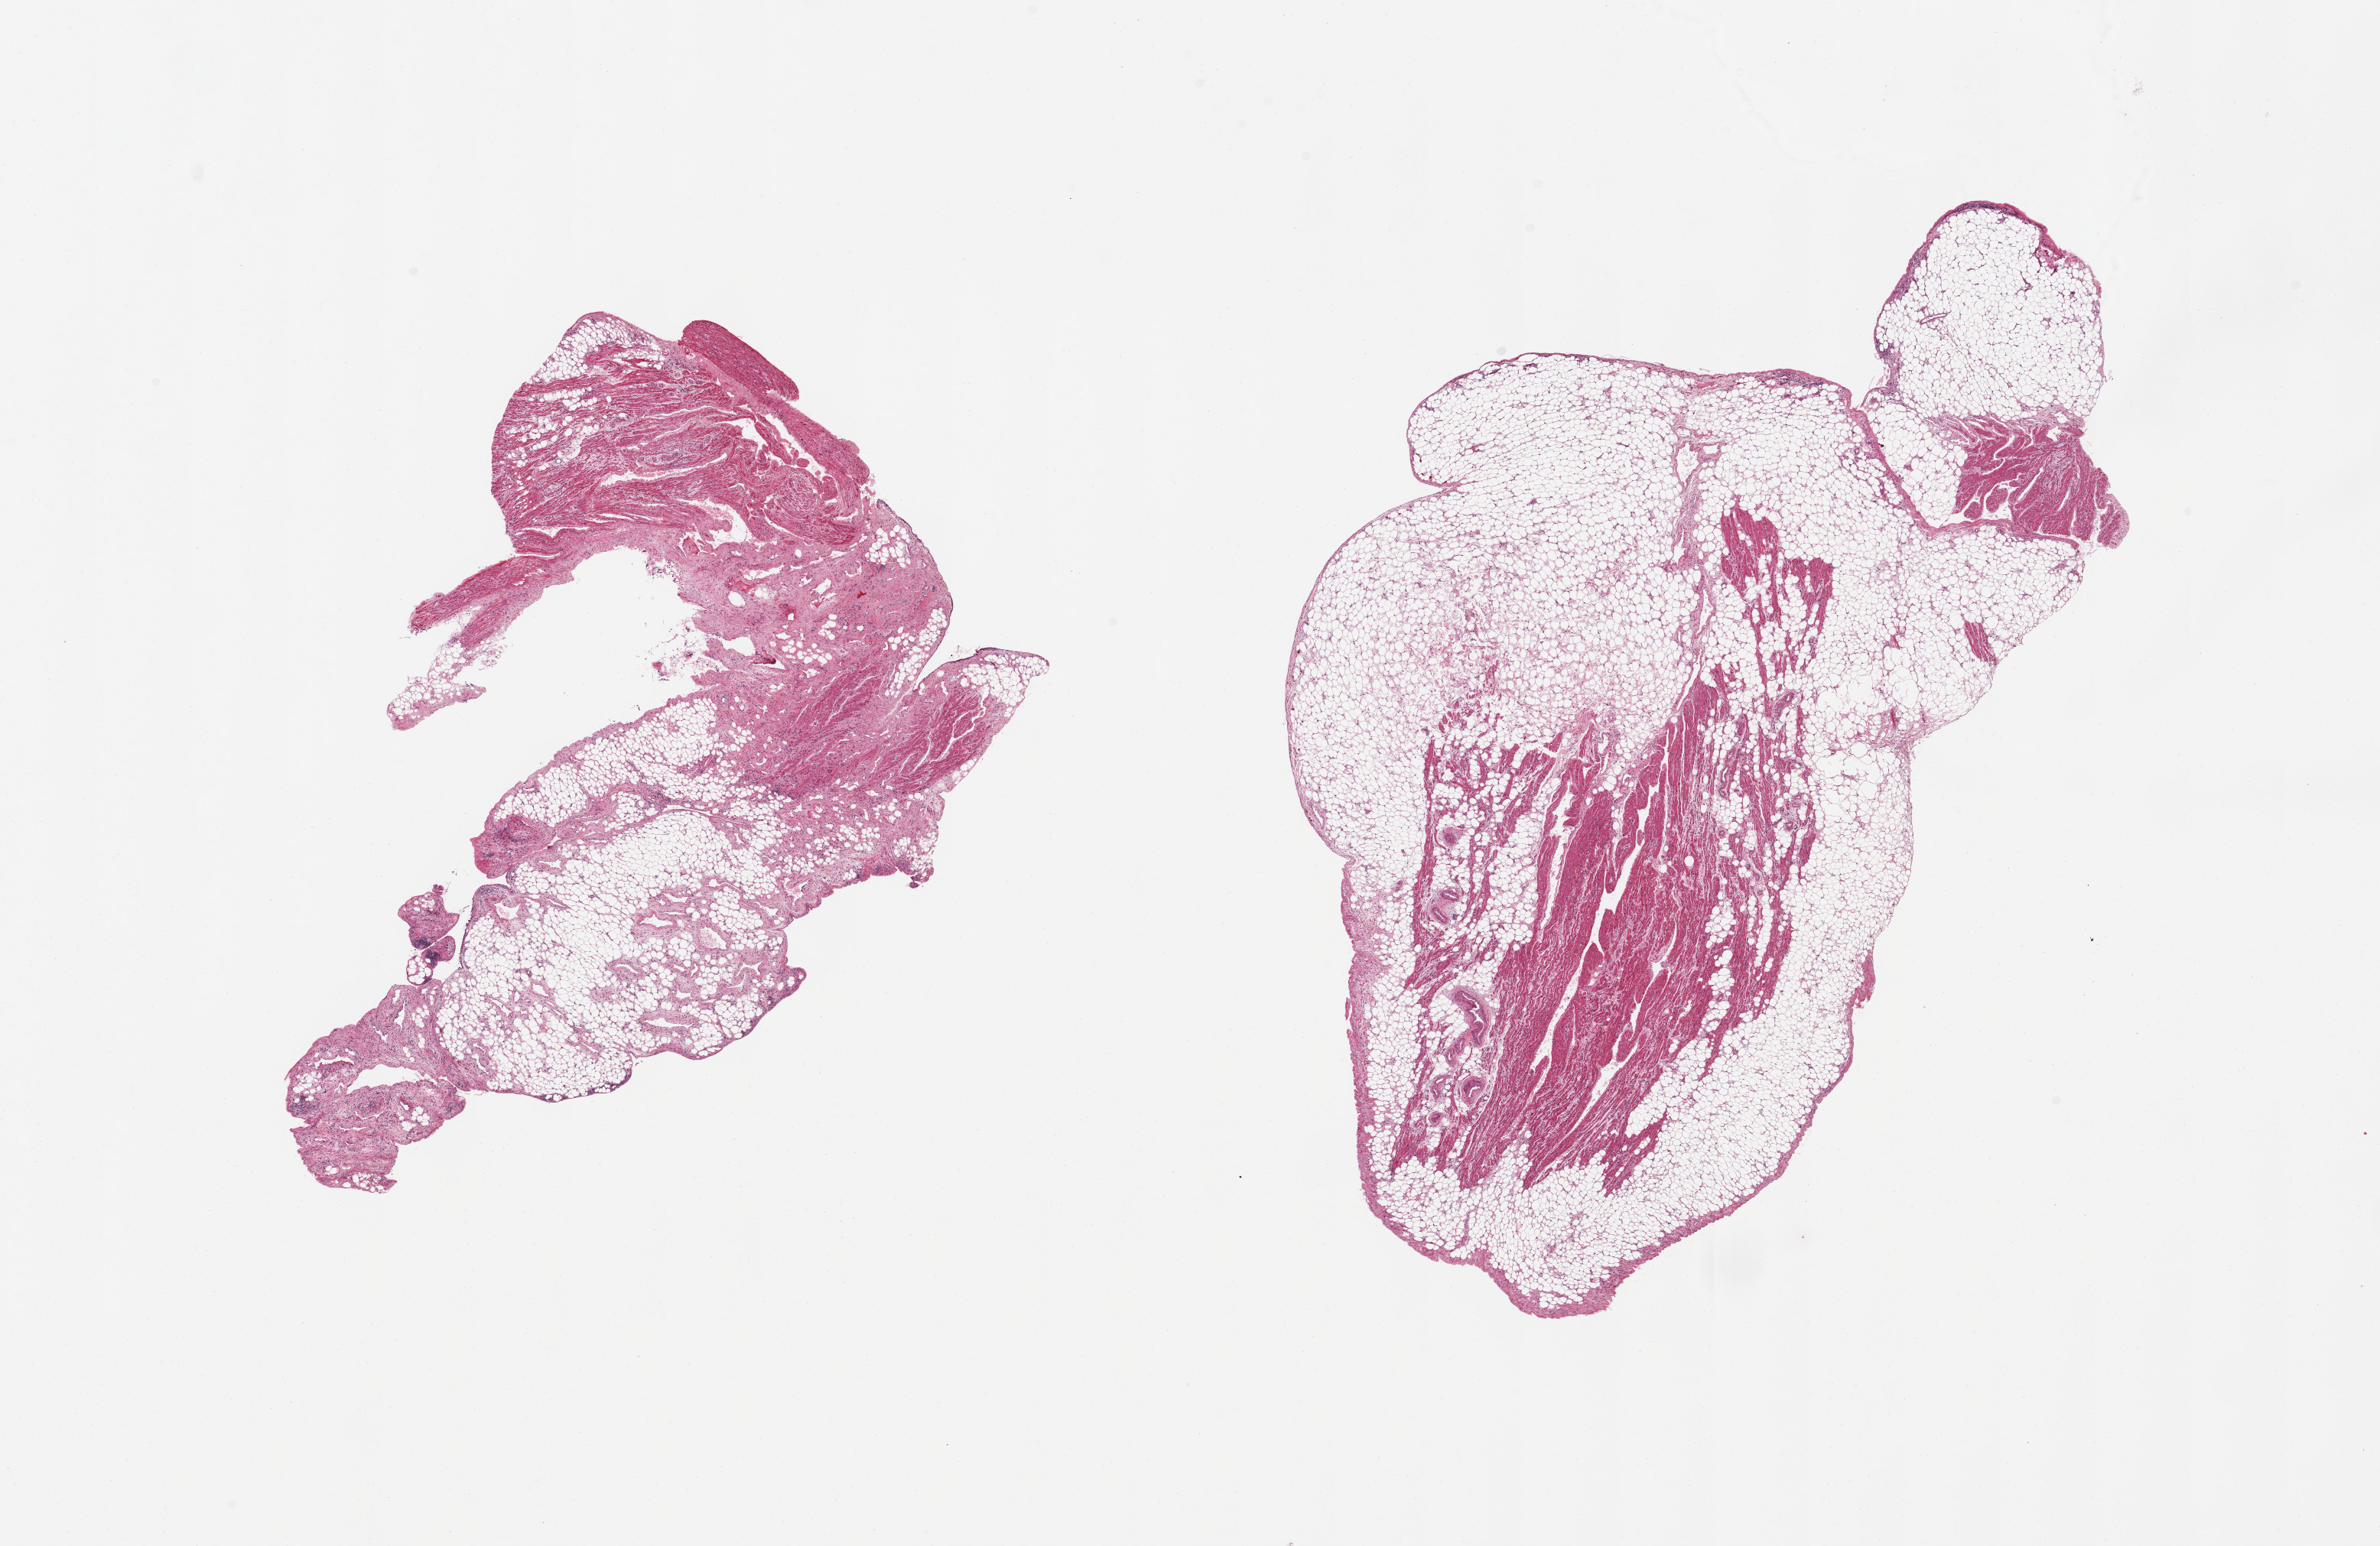
Whole-slide image, haematoxylin and eosin stain, brightfield, a low-resolution overview of the entire scanned area, about 24.6 x 16.0 mm. PAXgene-fixed, paraffin-embedded tissue. Sampled site (target tissue): auricular appendage. Donor tissue sample. Donor sex: female.
Pathologist's review note for this sample: 2 pieces, ~50% adherent/interstitial fat.